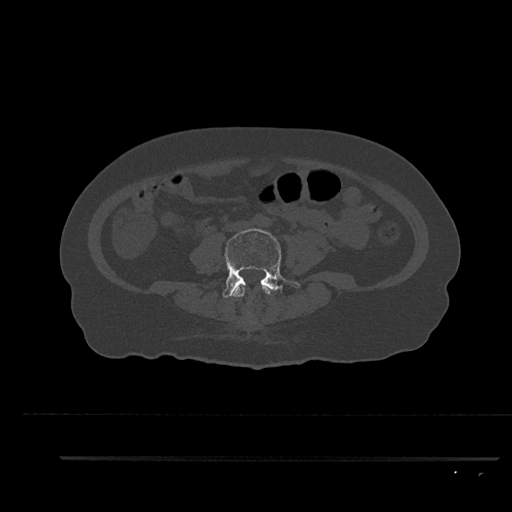
CT including the spine, one axial slice. Reconstruction kernel Br40s/3. Bone window (W 1800 / L 400 HU). 512 × 512 image matrix, field of view 408 × 408 mm. Female patient, age 44 years. From the clinical record (not read from this slice): primary cancer: renal; vertebrae with lytic lesions (as recorded): L1.
Structures marked on this image (semi-automatic segmentation, software-assisted and operator-edited):
- L3 vertebra: box from (x=232, y=284) to (x=271, y=297) px
- L4 vertebra: (x=222, y=228)–(x=300, y=298)